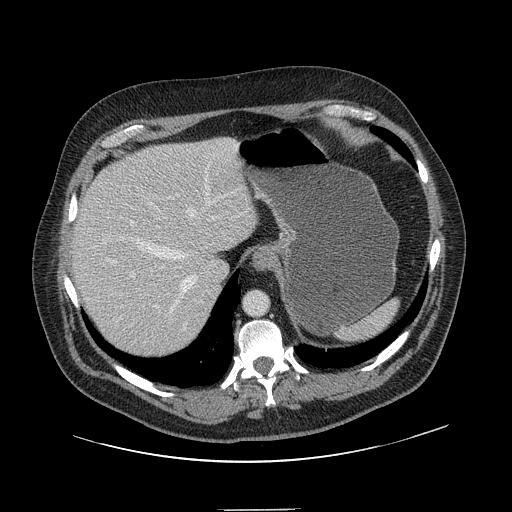
Contrast-enhanced abdominal CT, one axial slice; position 116 of 154 along the scan axis; intravenous contrast given; soft-tissue window (W 400 / L 40 HU); 2.5 mm slice thickness; 512 × 512 image matrix, field of view 451 × 451 mm. Male patient, age 61 years. Case-level facts recorded for this patient, not image findings: diagnosis: colorectal cancer liver metastases, imaged before liver resection; multiple liver metastases: yes; largest metastasis: 2.6 cm; disease in both lobes: yes.
Structures marked on this image (expert manual segmentation):
- hepatic veins: bounding box (x1, y1, x2, y2) in pixels: (135, 193, 225, 311)
- liver: (71, 139, 258, 359)
- planned liver remnant (the part of the liver to remain after resection): (71, 143, 258, 354)
- portal vein (with intrahepatic branches): (130, 216, 217, 308)